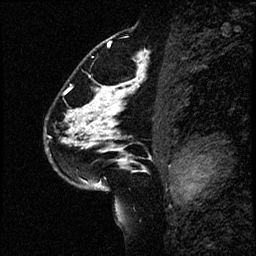
Breast MRI (dynamic contrast-enhanced), one sagittal slice; position 38 of 60 along the scan axis; dynamic contrast-enhanced study with each time point stored as its own series, time point 2 of 4 at this slice position (early post-contrast, ordered by acquisition time); 1.5 T; TE 4.2 ms, TR 17.6 ms; 2 mm slice thickness; 256 × 256 image matrix, field of view 200 × 200 mm. Patient: female, 43 years. From the clinical record (not read from this slice): setting: breast cancer imaged before/during neoadjuvant chemotherapy.
Outlined on this slice (semi-automatically segmented with operator editing):
- analysis volume of interest (the breast-tissue region the enhancement analysis was run in; not a lesion): bounding box [x1, y1, x2, y2] px = [47, 56, 169, 191]
- tumour enhancement mask (voxels above the 100 % enhancement threshold inside the analysis volume of interest): [67, 57, 138, 185]